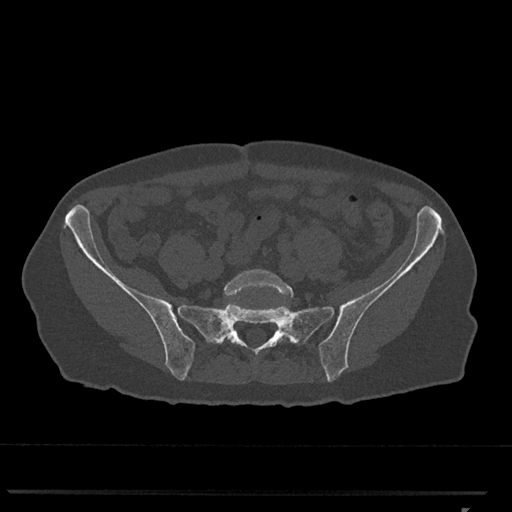
CT including the spine, one axial slice; reconstruction kernel Br40s/3; bone window (W 1800 / L 400 HU); 512 × 512 image matrix, field of view 380 × 380 mm. Female patient, age 62 years. Case-level facts recorded for this patient, not image findings: primary cancer: renal.
Structures marked on this image (semi-automatically segmented with operator editing):
- L5 vertebra: bounding box (x1, y1, x2, y2) in pixels: (224, 269, 294, 340)